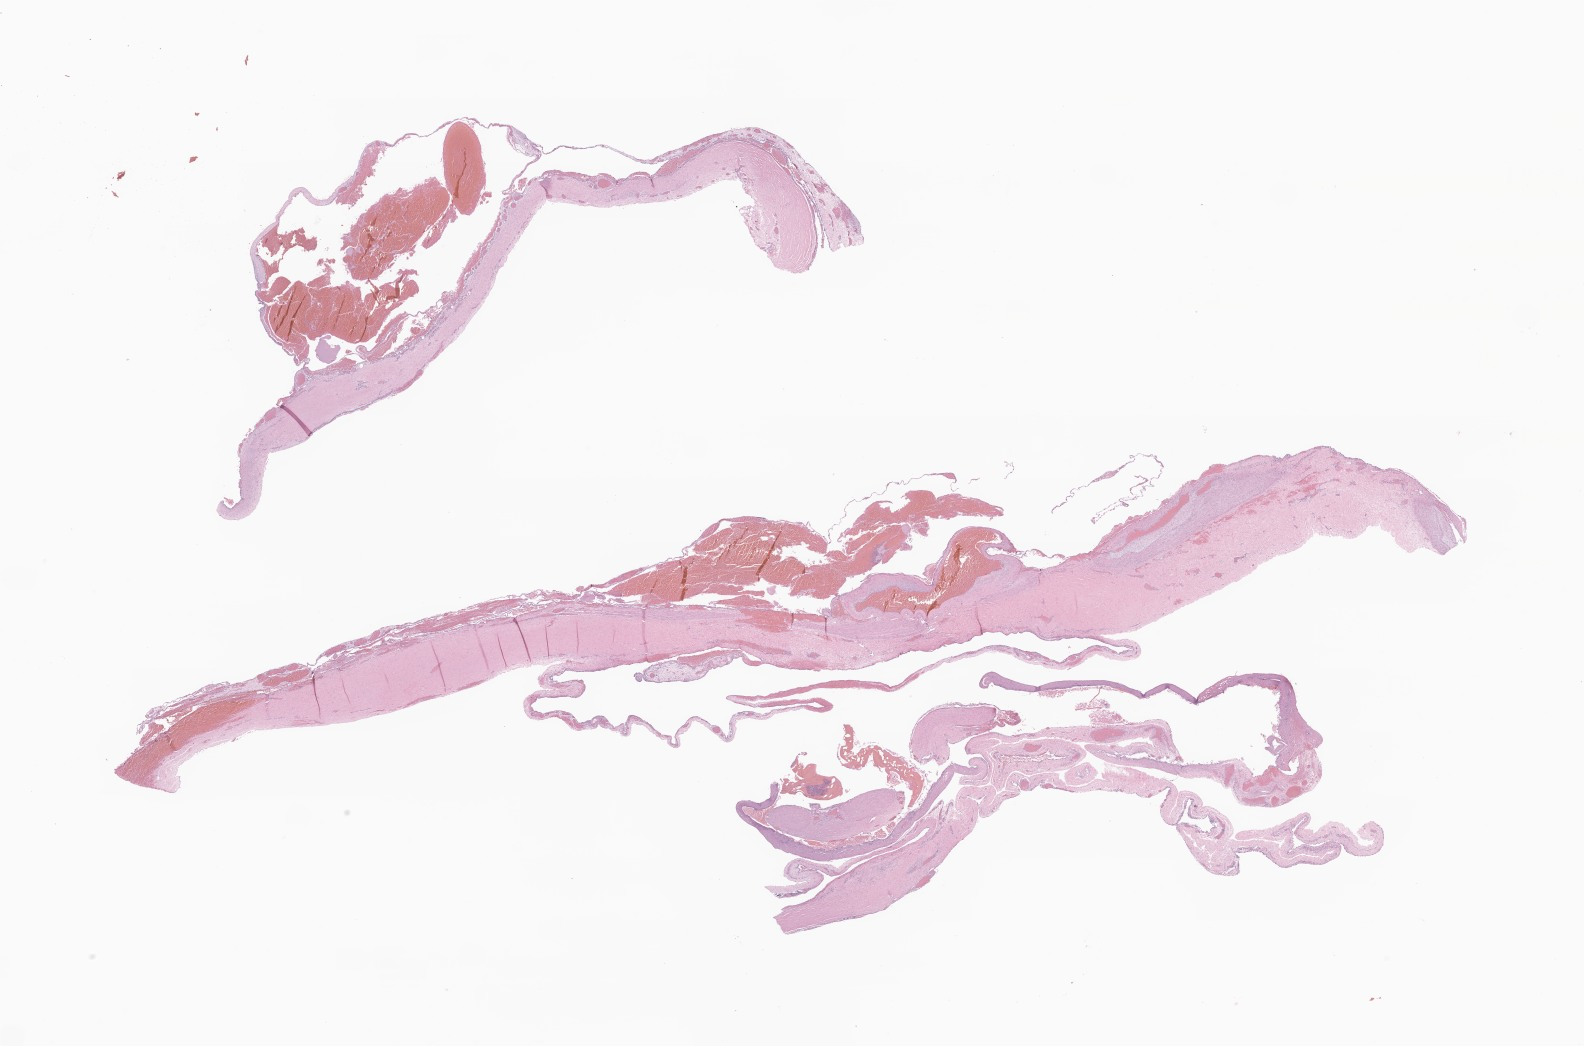
Digitized hematoxylin and eosin (H&E)-stained section of tumor tissue from the upper lobe of lung, whole scanned area (about 26.7 x 17.6 mm) shown as a low-resolution overview; formalin-fixed, paraffin-embedded (FFPE) tissue. Patient: male, age 37 months (3 years 1 month).
• recorded diagnosis: Pleuropulmonary blastoma